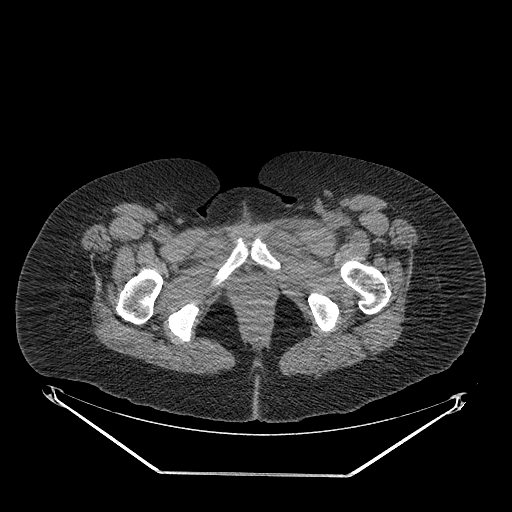
CT of an extremity soft-tissue mass (from a PET/CT study), one axial slice; position 50 of 267 along the scan axis; reconstruction kernel STANDARD; soft-tissue window (W 400 / L 40 HU); 3.75 mm slice thickness; 512 × 512 image matrix, field of view 500 × 500 mm. Female patient. Case-level facts recorded for this patient, not image findings: histological type: myxofibrosarcoma; grade: intermediate; site of the primary tumour: left thigh.
Outlined on this slice (expert contour drawn on MRI and transferred to this co-registered scan by the dataset authors):
- gross tumour volume including surrounding oedema: box from (x=269, y=210) to (x=359, y=250) px